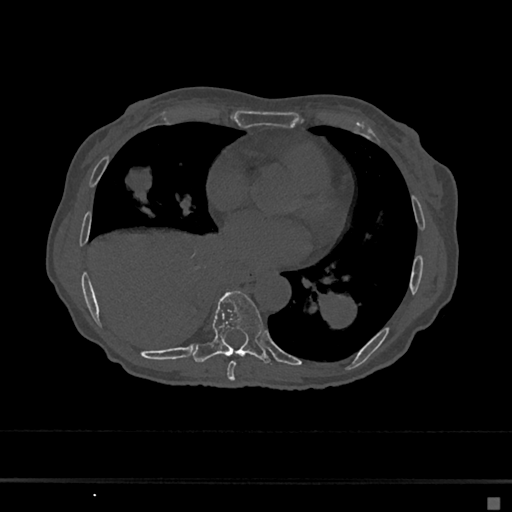
CT including the spine, one axial slice; position 333 of 797 along the scan axis; 120 kVp; bone window (W 1800 / L 400 HU); 0.5 mm slice thickness; 512 × 512 image matrix. Patient: female, 68 years. Case-level facts recorded for this patient, not image findings: primary cancer: renal.
Structures marked on this image (semi-automatically segmented with operator editing):
- T7 vertebra: bounding box [x1, y1, x2, y2] px = [227, 361, 236, 381]
- T8 vertebra: [193, 291, 271, 364]